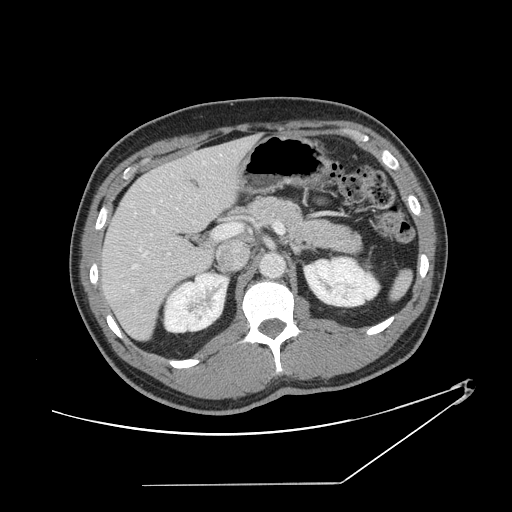
Contrast-enhanced abdominal CT, one axial slice. Position 79 of 152 along the scan axis. Reconstruction kernel STANDARD. Intravenous contrast given. Soft-tissue window (W 400 / L 40 HU). 2.5 mm slice thickness. 512 × 512 image matrix, field of view 432 × 432 mm. Male patient, age 45 years. Case-level facts recorded for this patient, not image findings: diagnosis: colorectal cancer liver metastases, imaged before liver resection.
Structures marked on this image (manually delineated by an expert):
- hepatic veins: box from (x=132, y=154) to (x=222, y=292) px
- liver: (x=102, y=138)–(x=254, y=339)
- planned liver remnant (the part of the liver to remain after resection): (x=102, y=157)–(x=214, y=339)
- portal vein (with intrahepatic branches): (x=132, y=222)–(x=284, y=269)